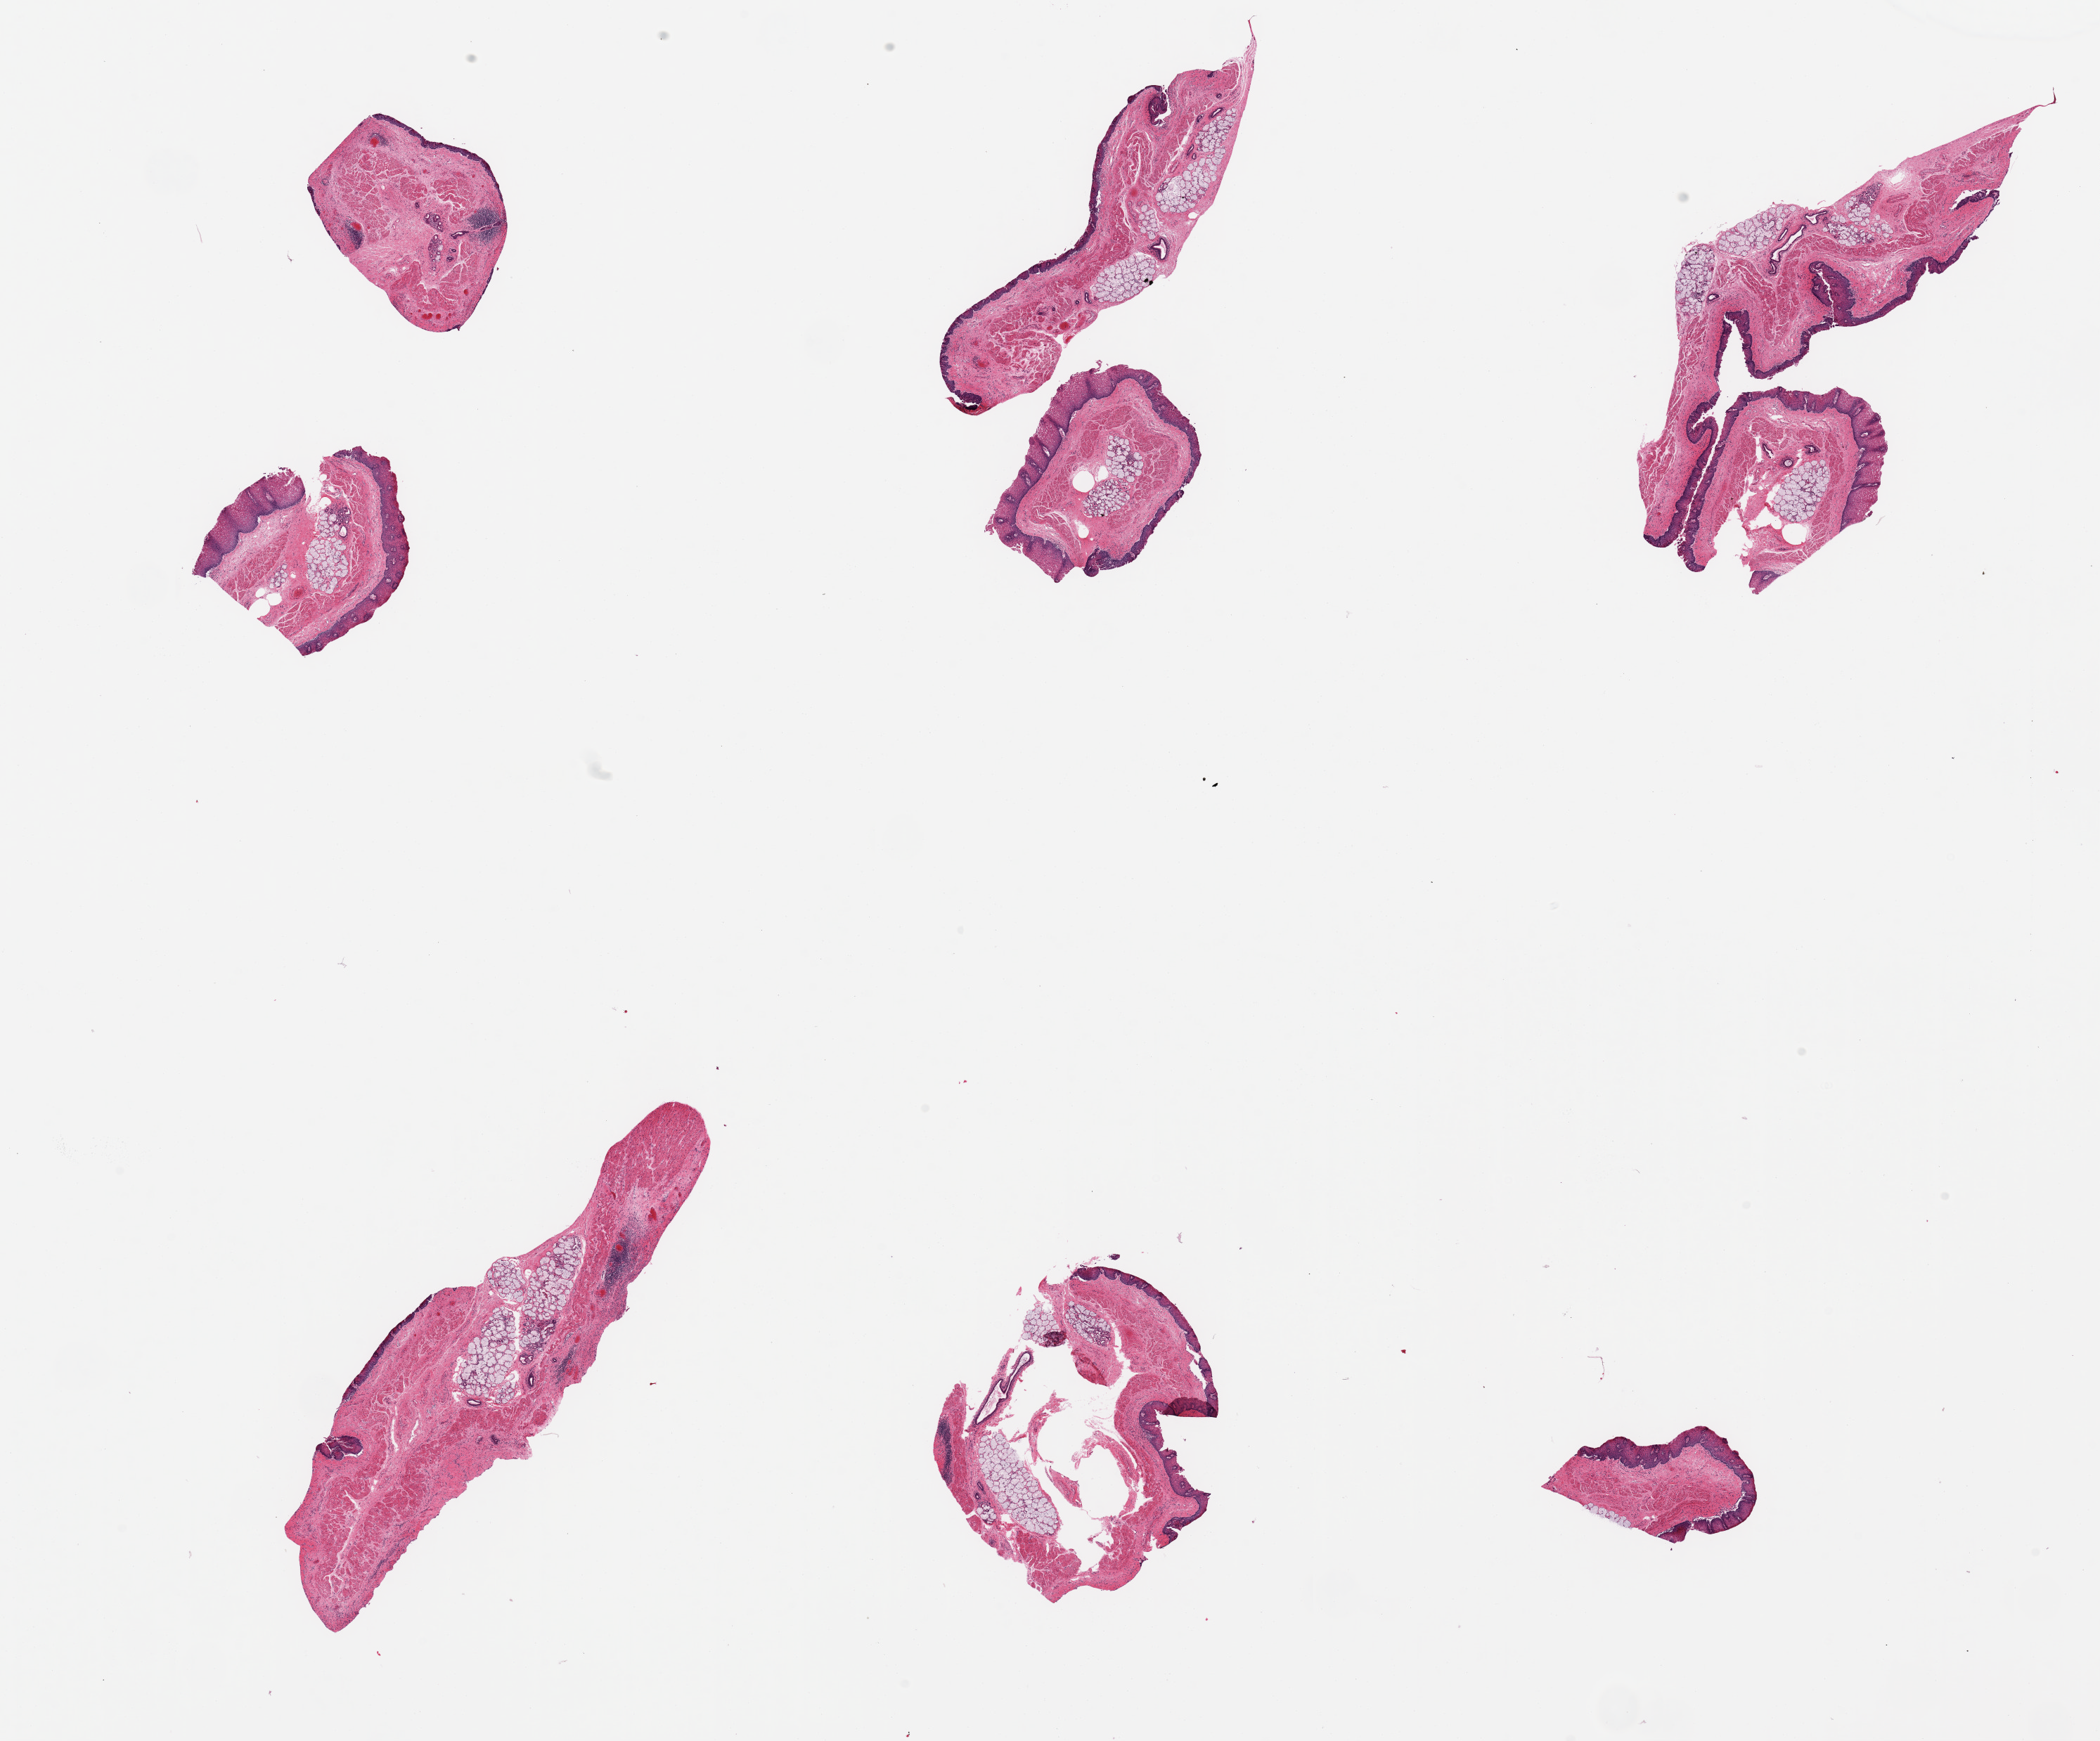
Hematoxylin and eosin (H&E) whole-slide image — shown as a low-resolution overview of the whole scanned area (about 23.6 x 19.6 mm); PAXgene-fixed paraffin-embedded (PFPE) section; target tissue: esophageal mucous membrane; tissue donor sample. Donor: male.
• reviewer comment on this tissue sample: 6 fragmented pieces; chronic esophagitis